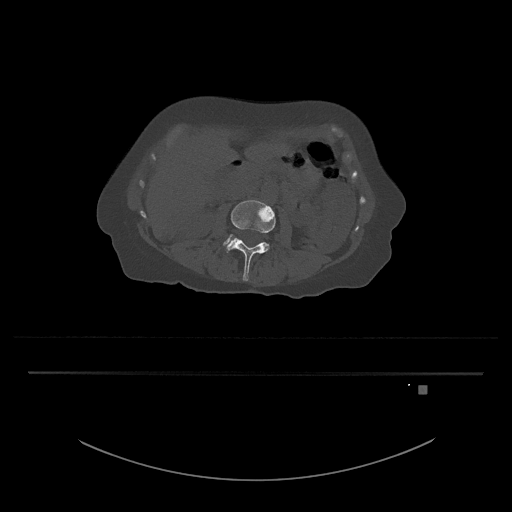
CT including the spine, one axial slice; slice 420 of 797 in the series (ordered by position); 120 kVp; bone window (W 1800 / L 400 HU); 0.5 mm slice thickness; 512 × 512 image matrix, field of view 500 × 500 mm. Patient: female, 57 years. Case-level facts recorded for this patient, not image findings: primary cancer: cervical.
Structures marked on this image (semi-automatic segmentation, software-assisted and operator-edited):
- L3 vertebra: box from (x=224, y=200) to (x=276, y=281) px
- L4 vertebra: (x=224, y=239)–(x=229, y=245)